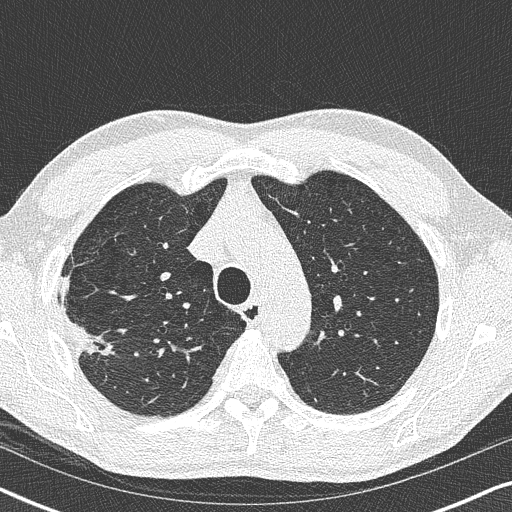
Low-dose screening chest CT, one axial slice. Slice 276 of 356 in the series (ordered by position). Lung window (W 1500 / L -600 HU). 1 mm slice thickness. 512 × 512 image matrix, field of view 330 × 330 mm.
Outlined on this slice (outlined manually by an expert reader):
- lesion 1 (tumor, upper lobe of right lung): box from (x=70, y=320) to (x=114, y=356) px